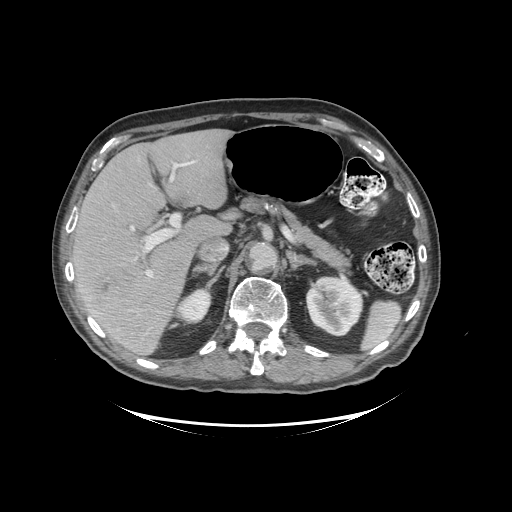
Contrast-enhanced abdominal CT (liver protocol), one axial slice. Slice 62 of 99 in the series (ordered by position). 140 kVp. Soft-tissue window (W 400 / L 40 HU). 512 × 512 image matrix, field of view 460 × 460 mm. From the clinical record (not read from this slice): diagnosis: hepatocellular carcinoma (patient treated with transarterial chemoembolisation; whether this scan precedes or follows treatment is not stated here); TNM stage (as recorded): Stage-I; Child-Pugh class: A; tumour differentiation: moderately differentiated.
Outlined on this slice (semi-automatically segmented with operator editing):
- liver parenchyma outside the tumour (the mass and vessels are separate outlines, so this box may not span the whole liver): bounding box <72,128,231,354> (left, top, right, bottom; pixels)
- mass: <79,266,159,351>
- liver vessels: <76,161,195,316>